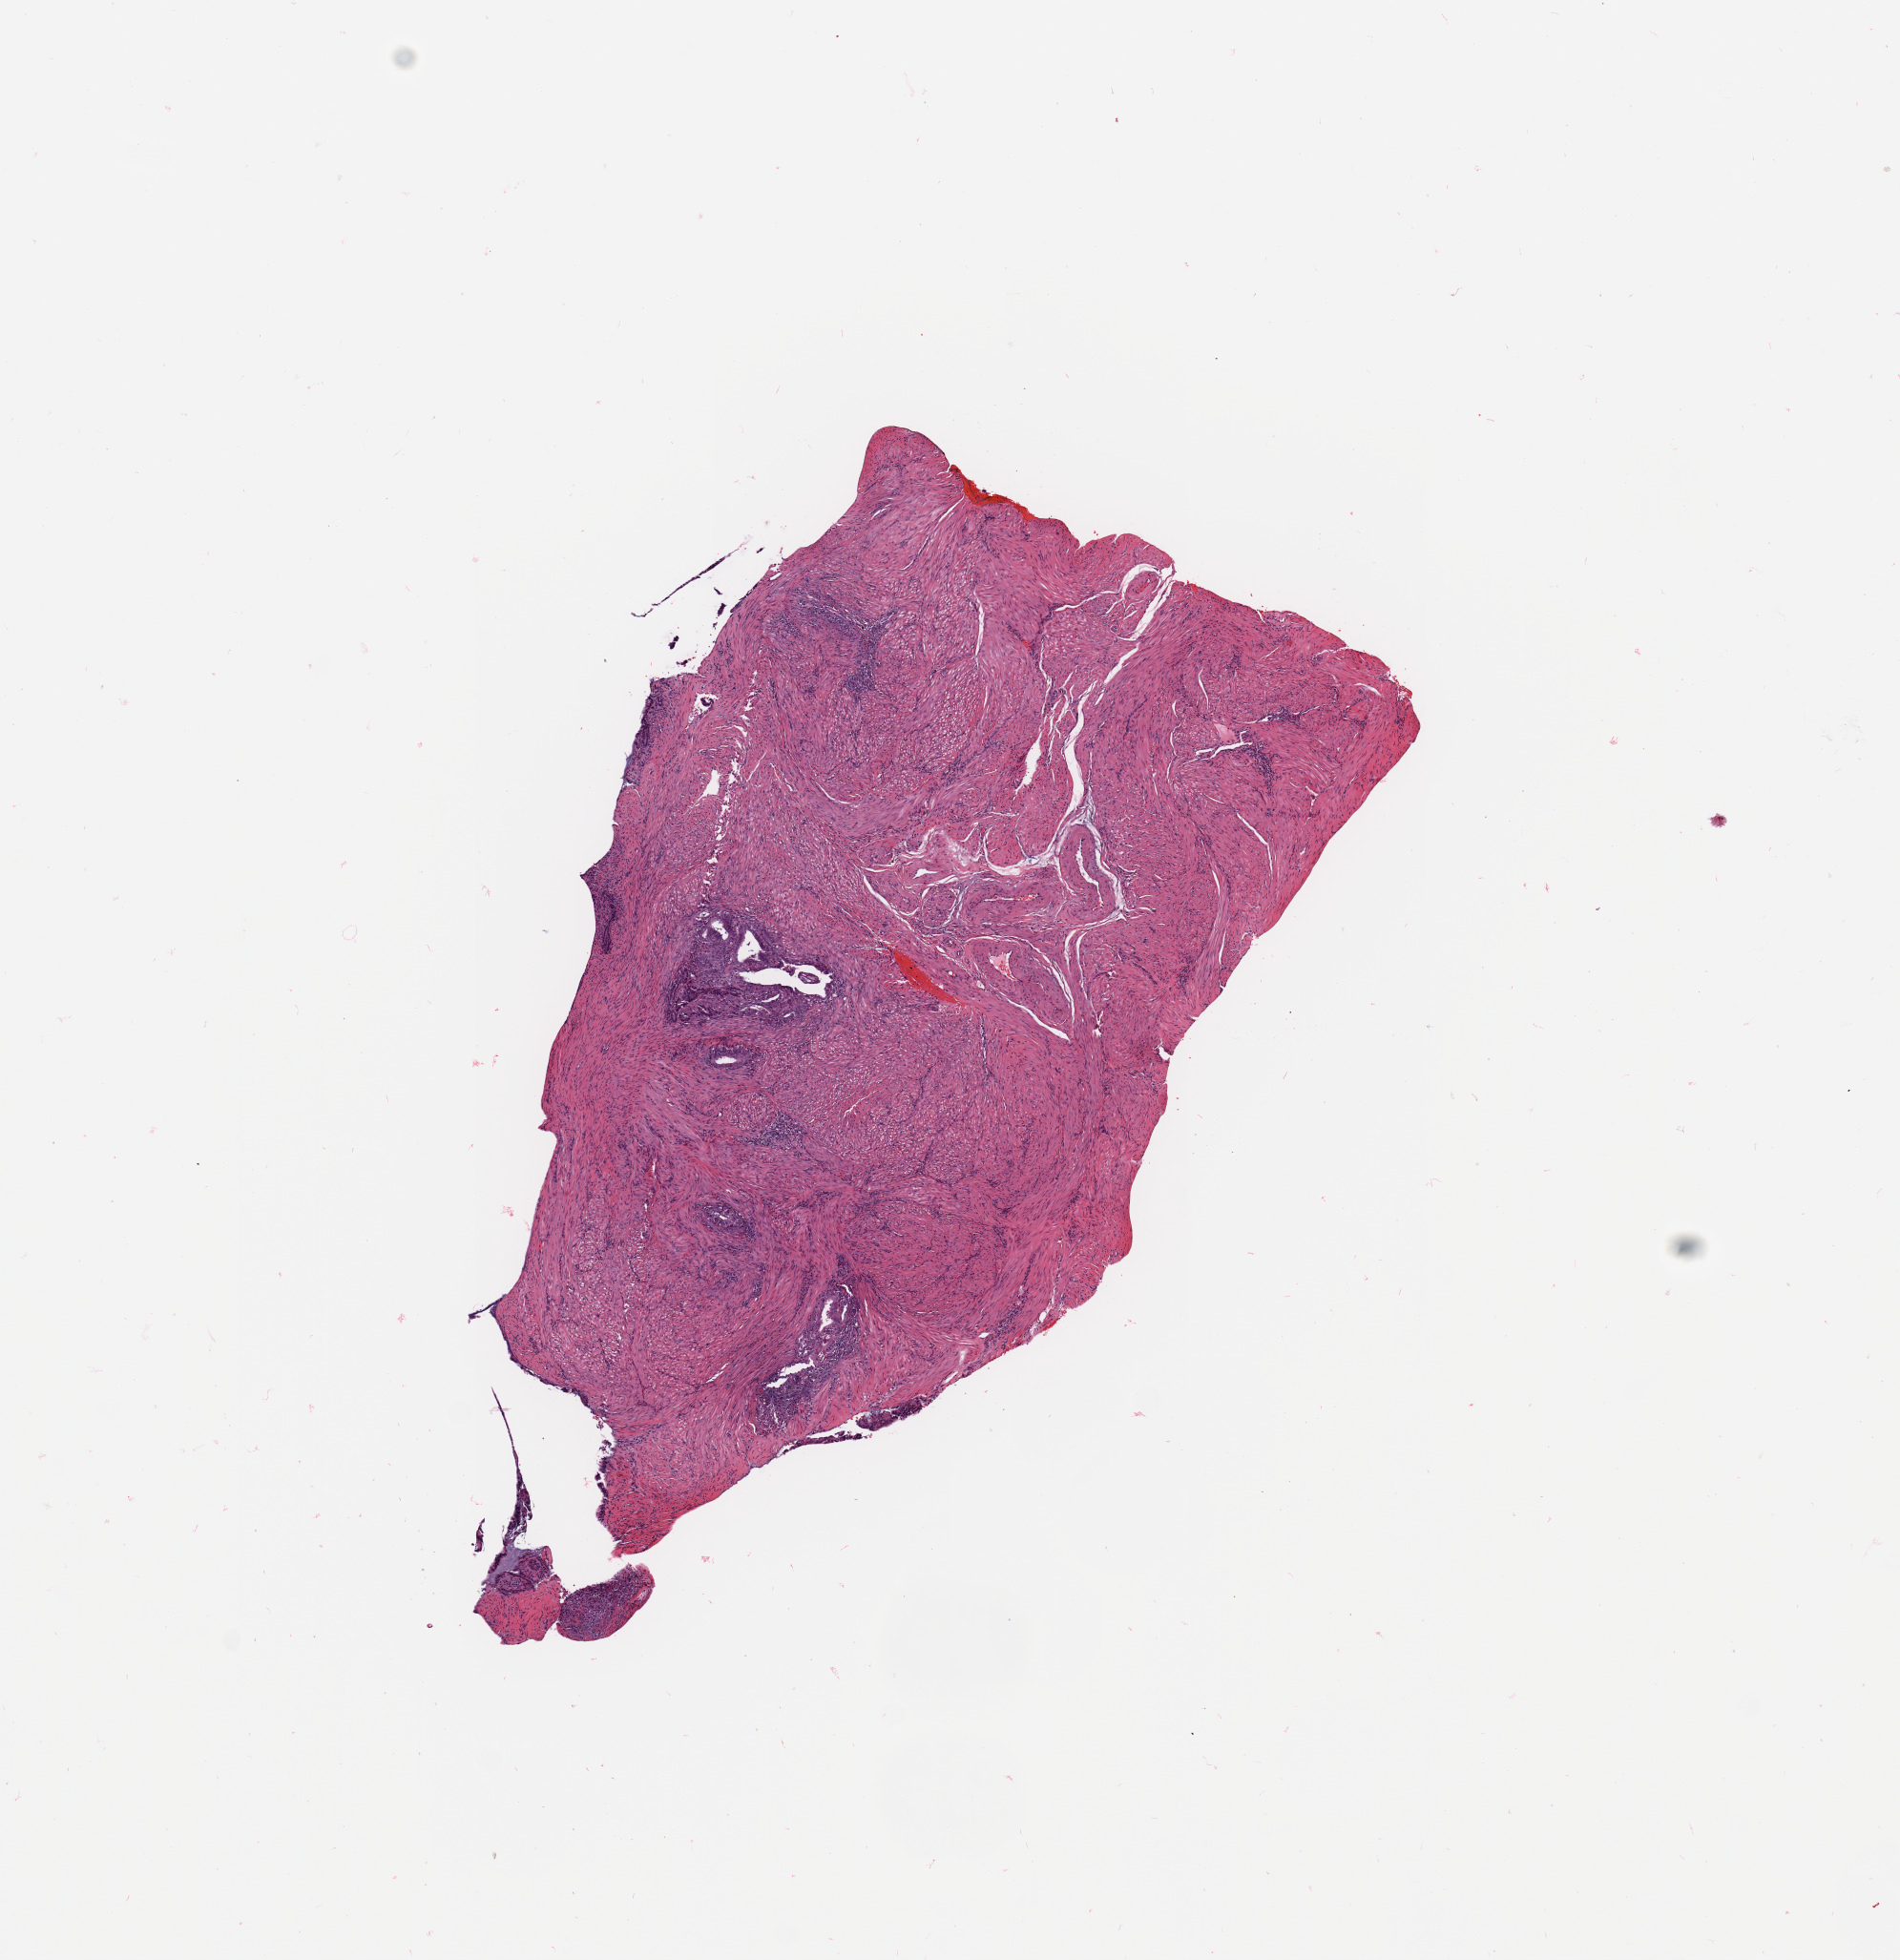
Digitized Hematoxylin and eosin (H&E) stained tissue section (whole slide) — low-resolution overview of the scanned area, about 7.9 x 8.1 mm (from a 20x scan); uterus, tumour tissue. Female, 56 y/o. Histologic grade: G1 (well differentiated).
* histologic diagnosis: Endometrioid adenocarcinoma, NOS
* AJCC pathologic stage: II